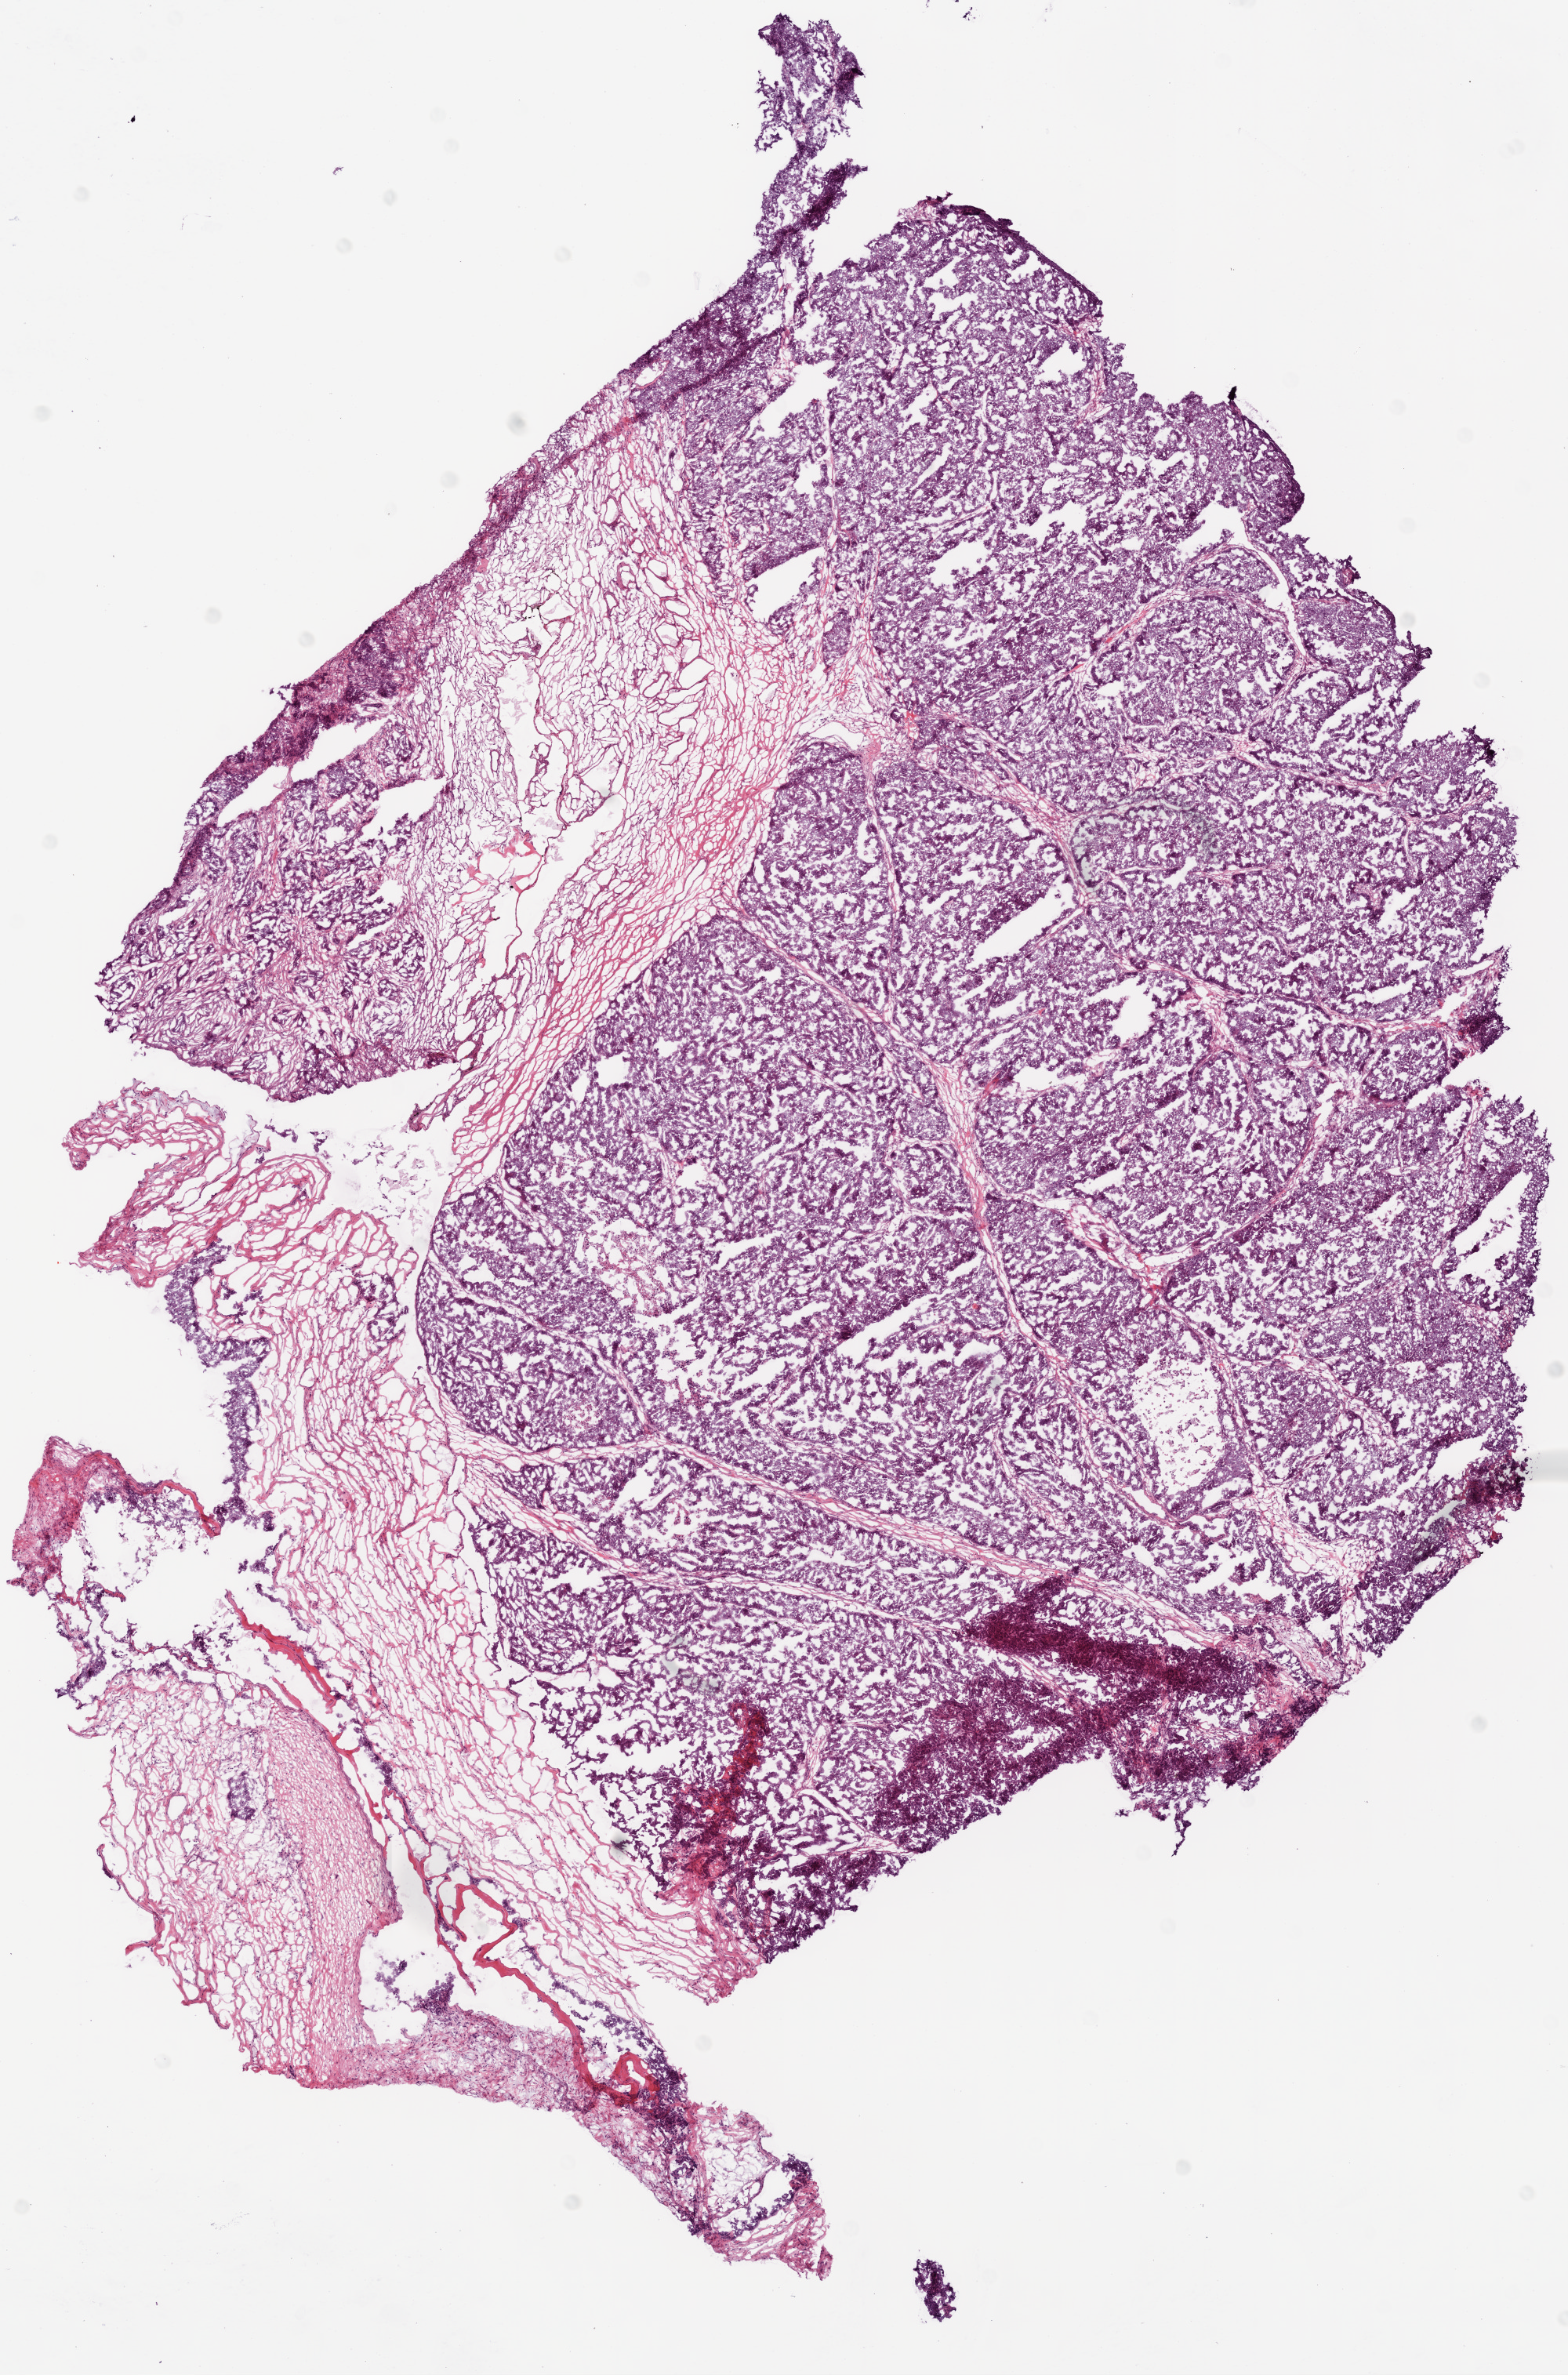
H&E whole-slide image — shown as a low-resolution overview of the whole scanned area (about 8.0 x 12.2 mm), frozen section from the bottom of the tissue portion, sample: primary tumour, ovary. Female, age 53 years at initial diagnosis. Histologic grade: G3 (poorly differentiated). Composition of this section per pathologist review: tumour cells 80%, tumour nuclei 90%, normal cells 0%, stromal cells 15%, necrosis 5%.
Histologic diagnosis: Serous cystadenocarcinoma, NOS. FIGO stage: IIIC. Laterality: bilateral.